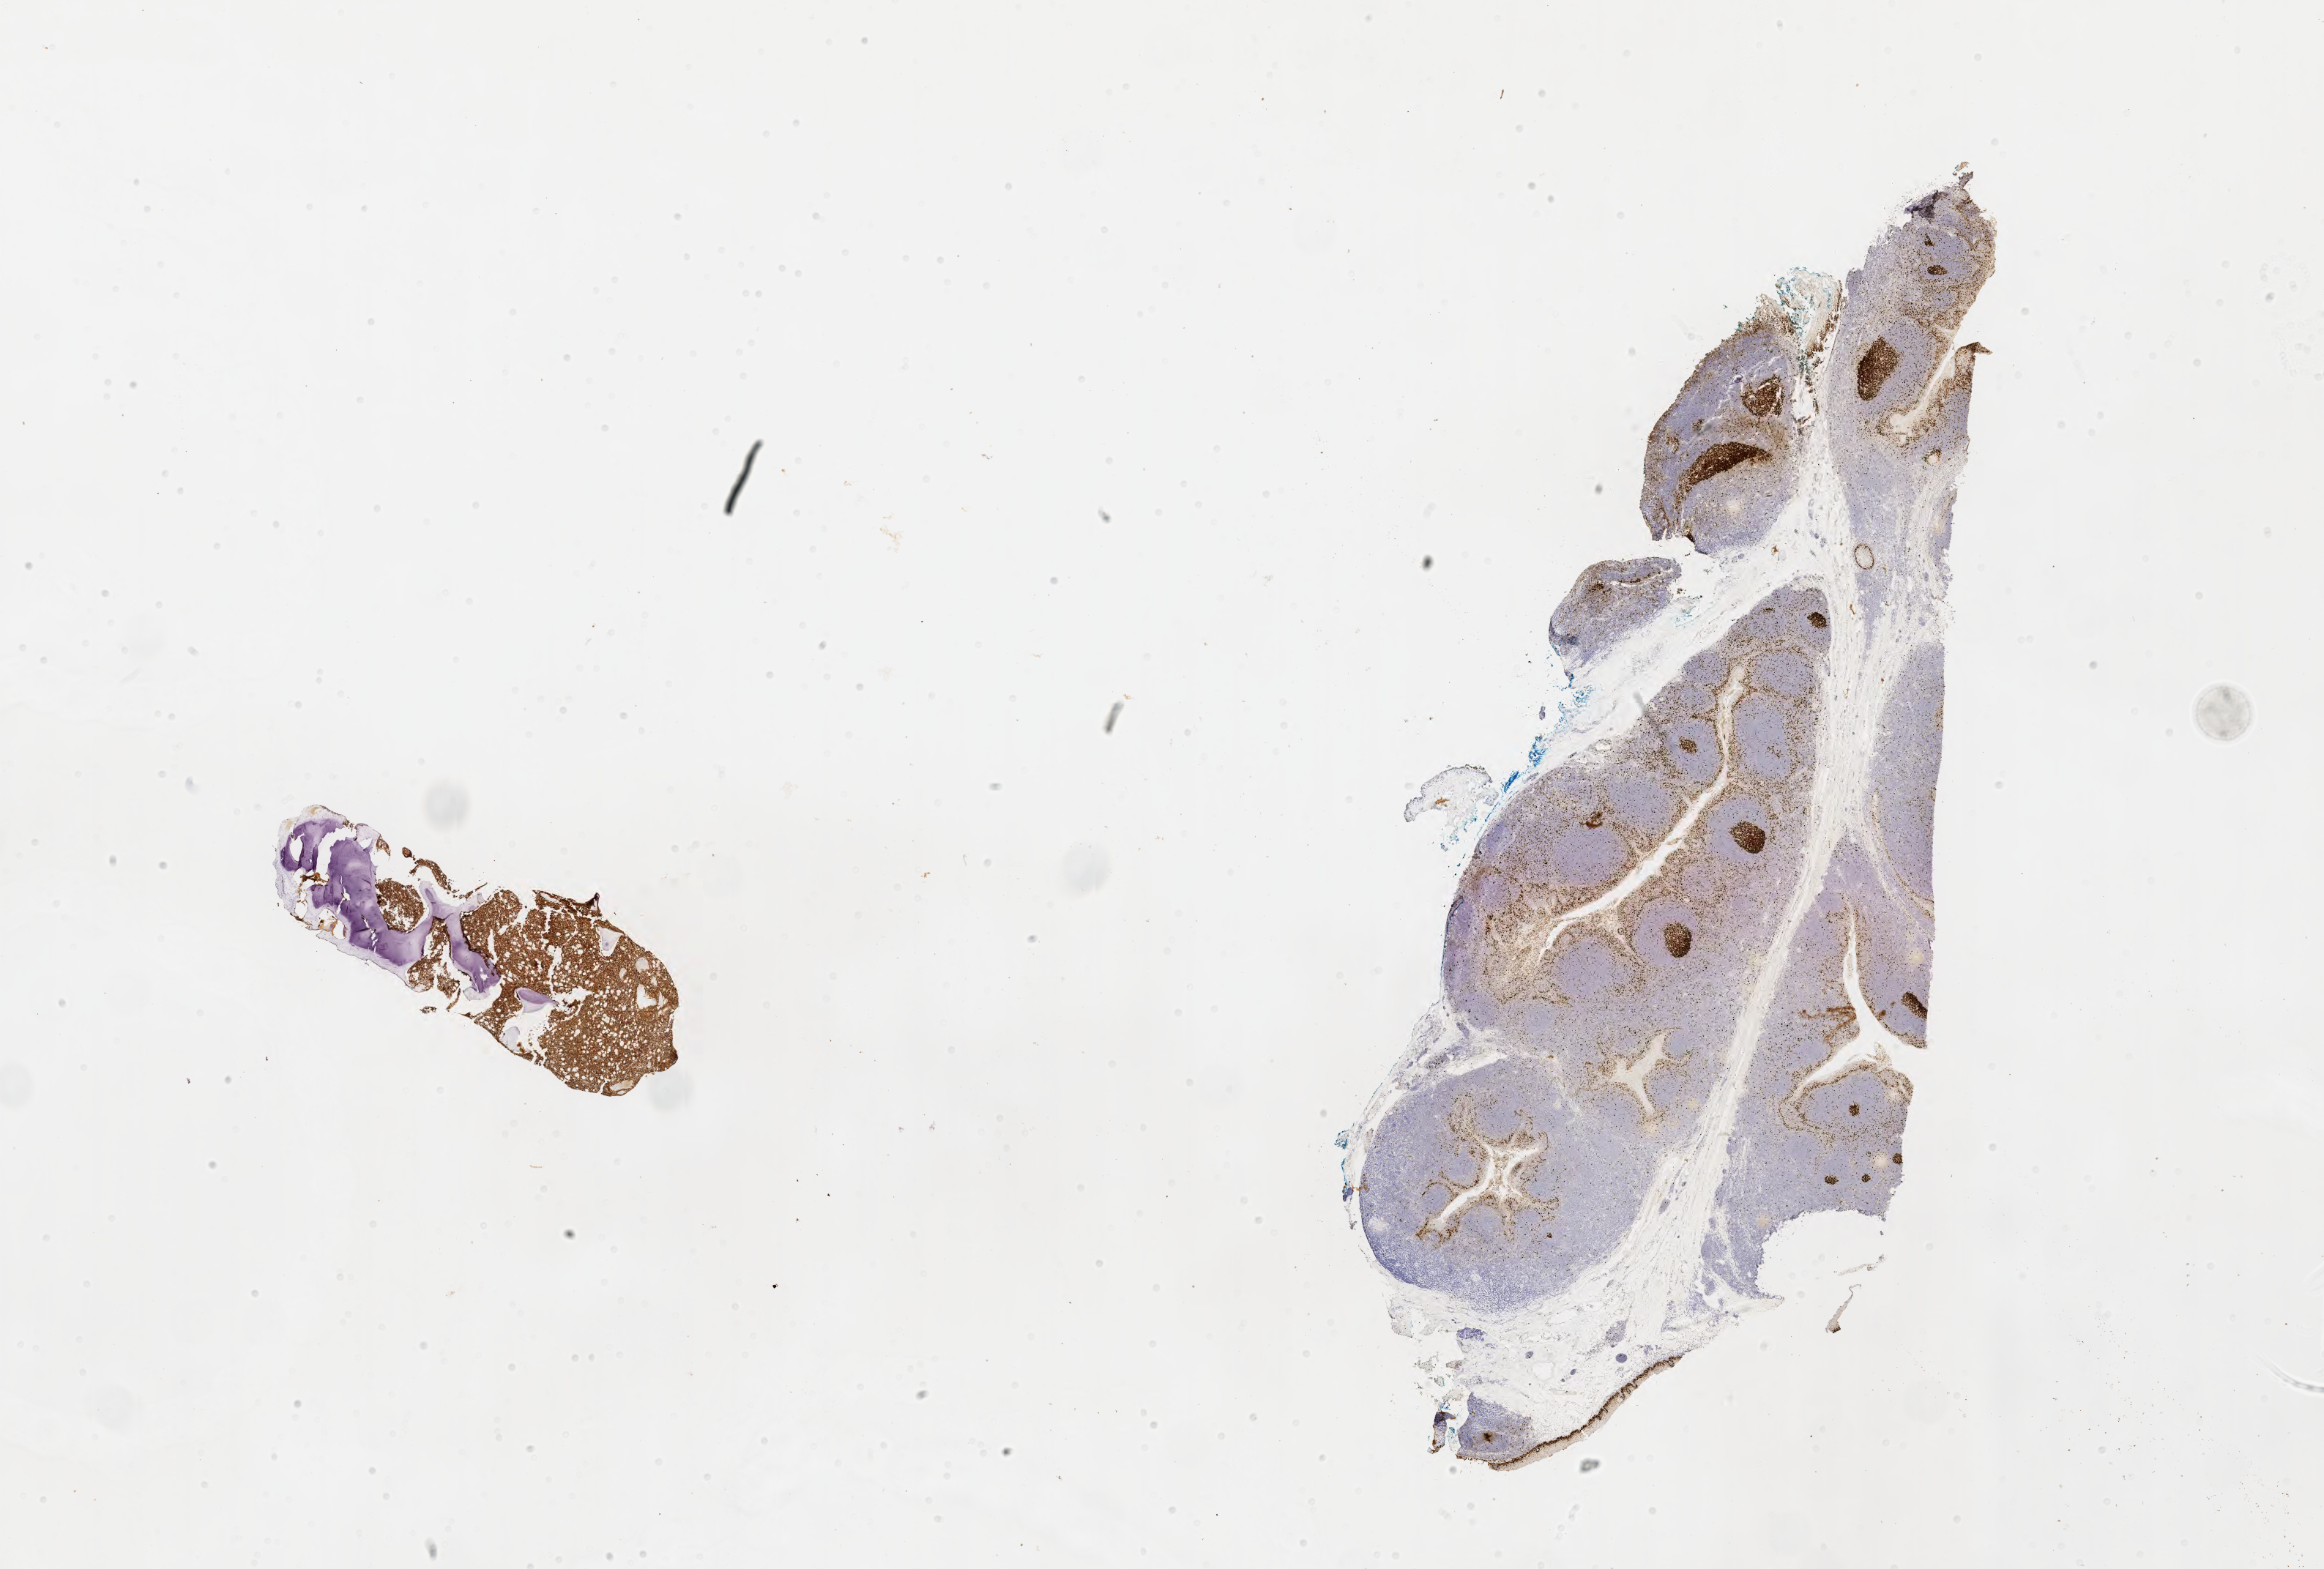
IHC for Ki-67, whole-slide image — a low-resolution overview of the entire scanned area, about 25.7 x 17.3 mm, tumor tissue, anatomic site: bone marrow. Male patient, age 15 years.
Histologic diagnosis: Burkitt lymphoma, NOS.